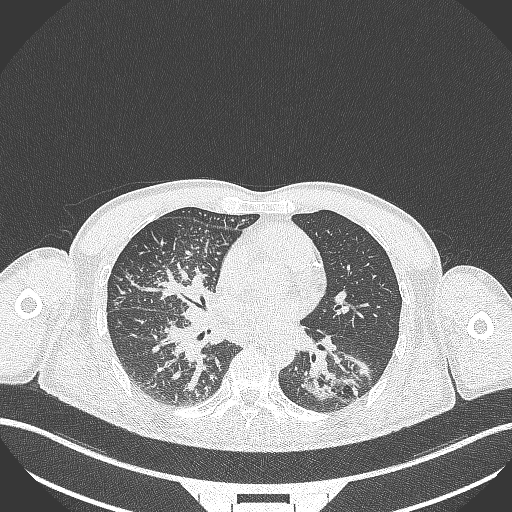
Chest CT, one axial slice; reconstruction kernel B70f; lung window (W 1500 / L -600 HU); 512 × 512 image matrix, field of view 400 × 400 mm. Male patient, age 49 years. From the clinical record (not read from this slice): clinical TNM (as recorded): T2b N1 M0.
Outlined on this slice (bounding box drawn by a radiologist):
- lung tumour (recorded histology: adenocarcinoma): bounding box (x1, y1, x2, y2) in pixels: (295, 362, 361, 407)